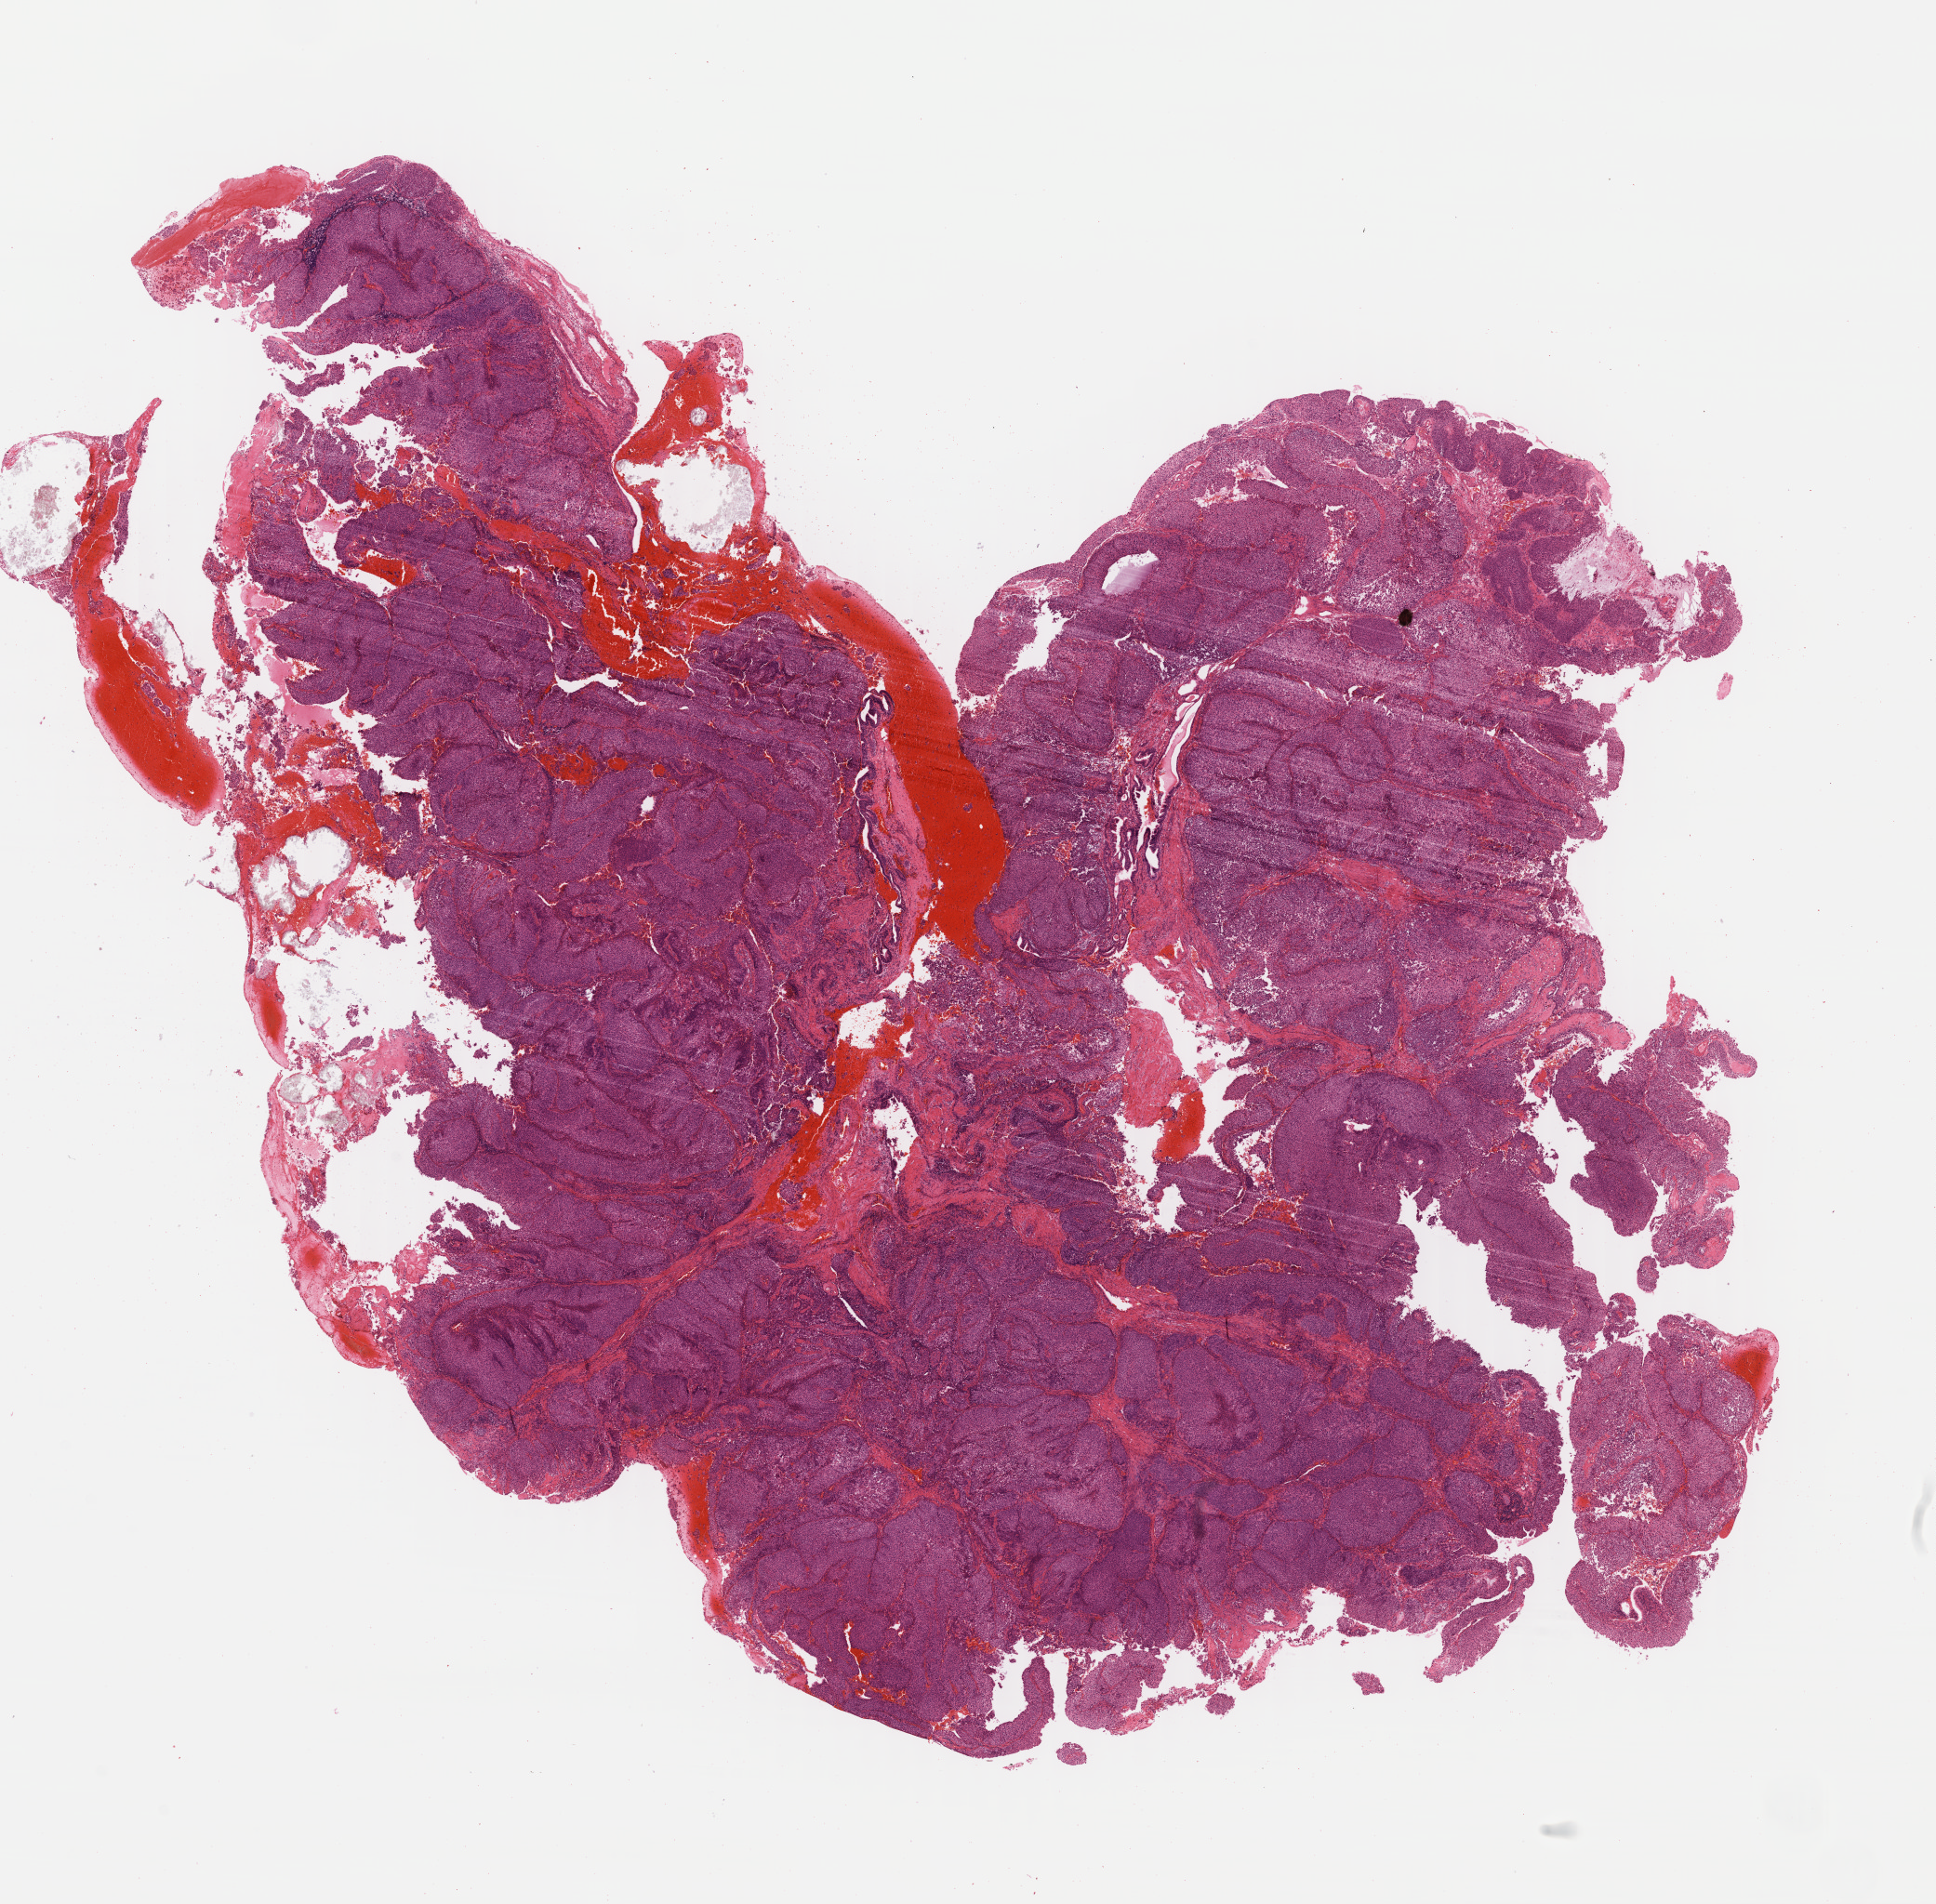
Hematoxylin and eosin (H&E) stained whole-slide image, shown as a low-resolution overview of the whole scanned area (about 16.4 x 16.1 mm, slide scanned at 40x), formalin-fixed paraffin-embedded (FFPE) diagnostic section, sample: primary tumour, bladder. Male, age 81 years at initial diagnosis. Histologic grade: low grade.
• histologic diagnosis: Transitional cell carcinoma
• TNM: T2b N0 M0
• AJCC pathologic stage: II